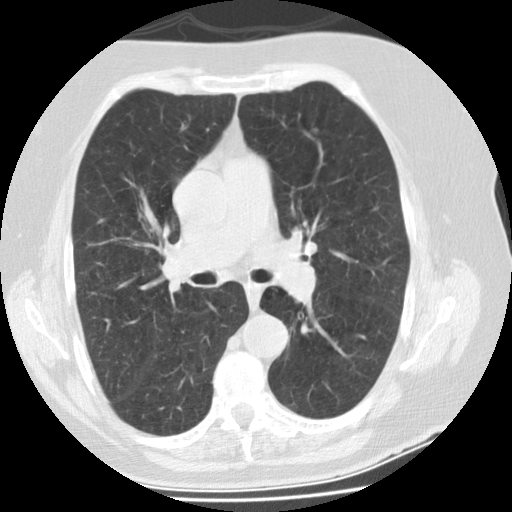
Chest CT (low-dose screening protocol), one axial image; second annual screen; lung window (W 1500 / L -600 HU); standard (soft-tissue) reconstruction kernel (STANDARD); 120 kVp; 512 × 512 image matrix, field of view 321 × 321 mm. Female, age 74 years at enrolment.
Lesion marked by an expert reader, bounding box (x1, y1, x2, y2) in pixels: (301, 118, 333, 145). The screening reader recorded 3 non-calcified nodules or masses ≥4 mm on this exam (right lower lobe, left upper lobe, left upper lobe); which of them this box marks is not recorded. Official screen result: positive, other. Lung cancer was diagnosed 68 days after this screen: bronchiolo-alveolar adenocarcinoma, NOS, left upper lobe, stage IA (AJCC 6th edition), 20 mm at pathology.